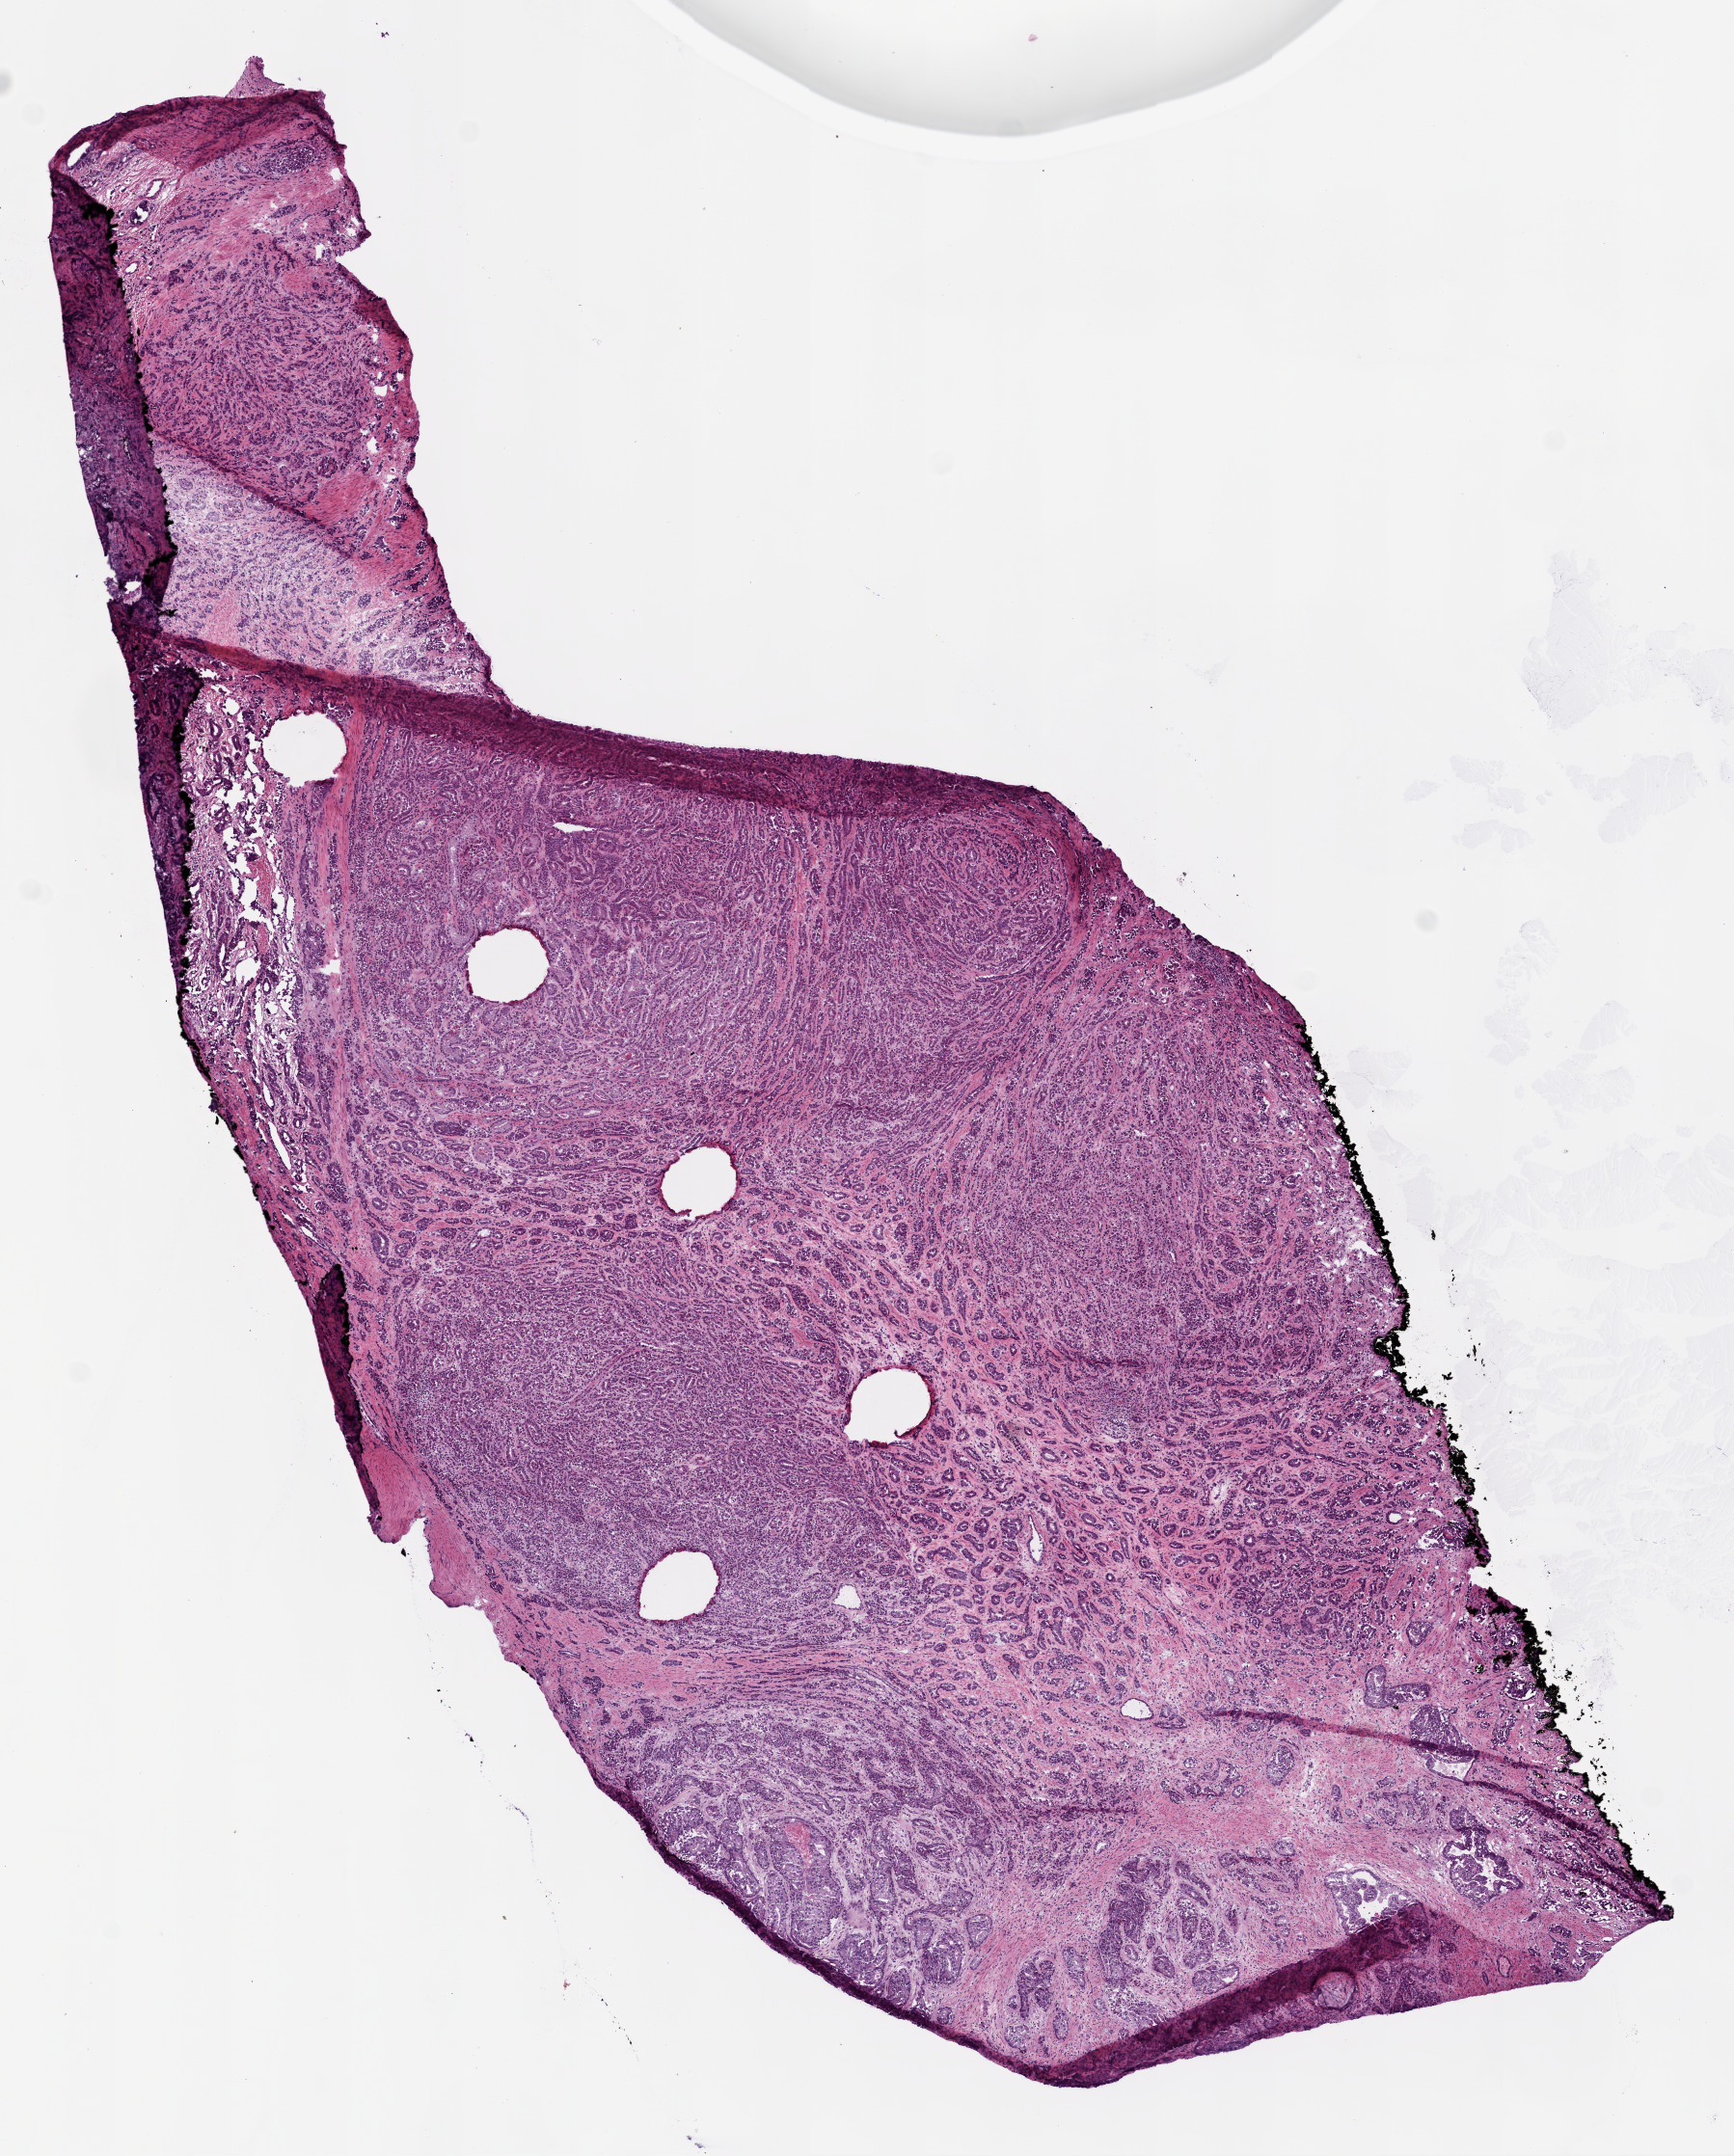
Whole-slide histology image, H&E-stained — whole scanned area (about 7.3 x 9.0 mm, slide scanned at 20x) shown as a low-resolution overview. Frozen section. Primary tumour sample from the prostate. Male, age 70 years at initial diagnosis. Composition of this section per pathologist review: tumour cells 0%, tumour nuclei 80%.
Pathologic diagnosis: Acinar cell carcinoma (prostate gland).